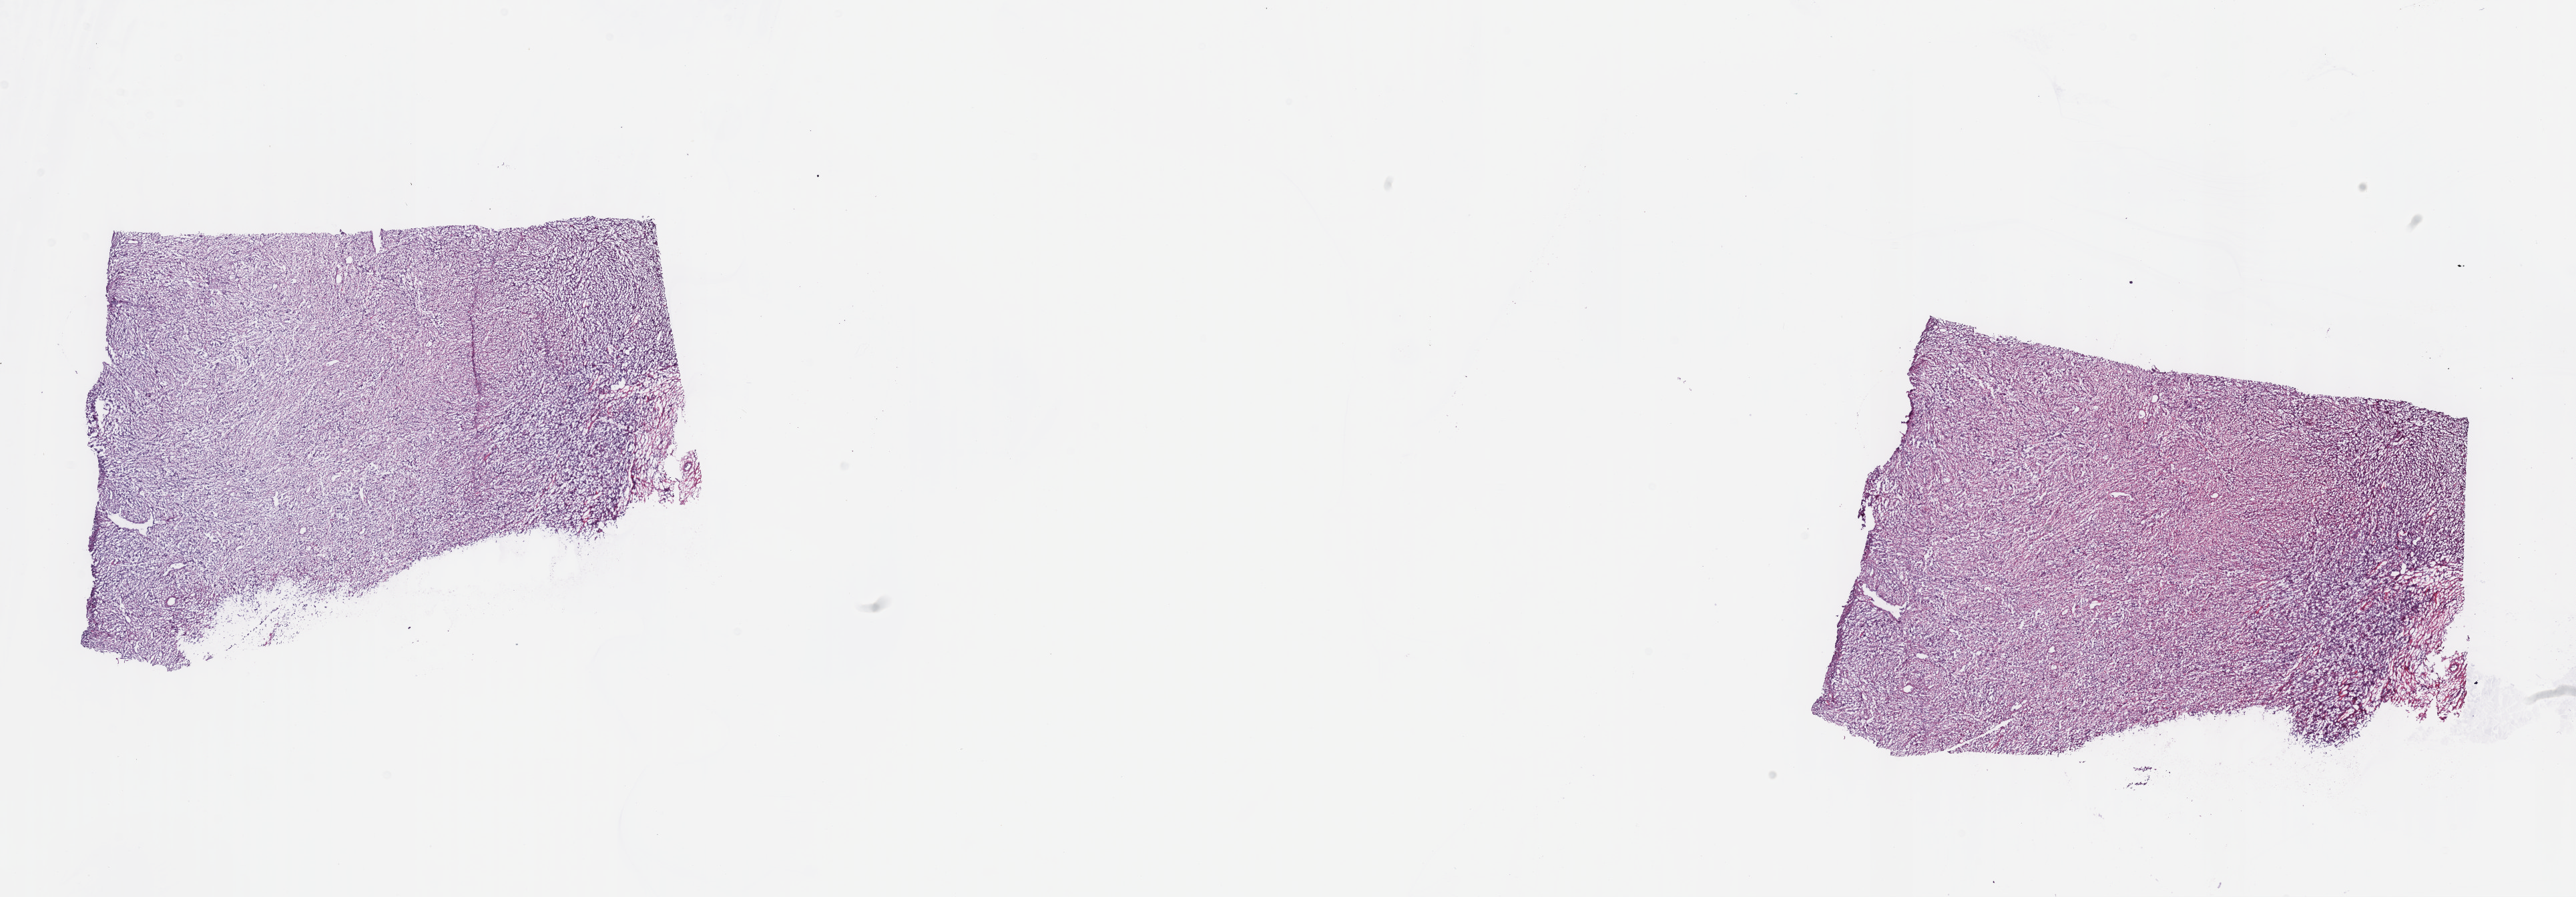
Hematoxylin and eosin (H&E) stained whole-slide image, shown as a low-resolution overview of the whole scanned area (about 31.2 x 10.9 mm, slide scanned at 40x), frozen section from the top of the tissue portion, sample: primary tumour, connective, subcutaneous and other soft tissues. Female, age 53 years at initial diagnosis. Slide review estimates, as recorded: tumour cells 90%, tumour nuclei 95%, normal cells 0%, stromal cells 10%, necrosis 0%. Infiltration values recorded for this section: lymphocyte infiltration 0%, monocyte infiltration 0%, neutrophil infiltration 0%.
Pathologic diagnosis: Leiomyosarcoma, NOS (connective, subcutaneous and other soft tissues, NOS).